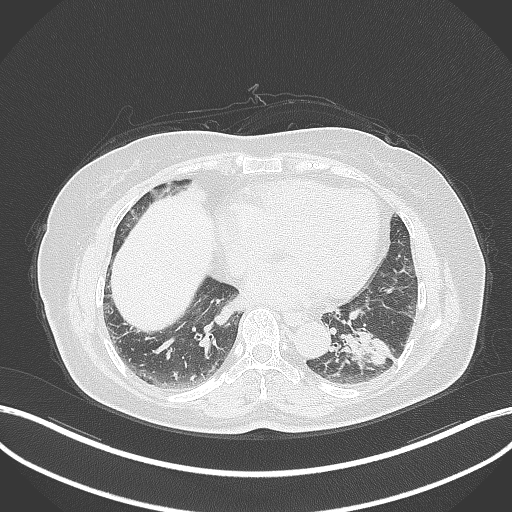
Chest CT, one axial slice; 120 kVp; lung window (W 1500 / L -600 HU); 512 × 512 image matrix, field of view 400 × 400 mm. Patient: female, 59 years. From the clinical record (not read from this slice): clinical TNM (as recorded): T2a N0 M0; histopathological grade: G2-3.
Outlined on this slice (rectangle marked by the reading radiologist):
- lung tumour (recorded histology: adenocarcinoma): bounding box [x1, y1, x2, y2] px = [336, 324, 394, 377]